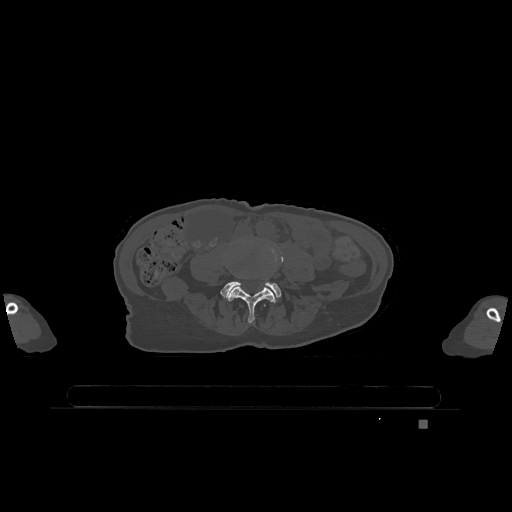
CT including the spine, one axial slice. Slice 276 of 1317 in the series (ordered by position). Bone window (W 1800 / L 400 HU). 0.5 mm slice thickness. 512 × 512 image matrix, field of view 500 × 500 mm. Patient: female, 74 years. Case-level facts recorded for this patient, not image findings: primary cancer: lung; vertebrae with lytic lesions (as recorded): T1, T4, T5, T6, L4, L5.
Structures marked on this image (semi-automatic segmentation, software-assisted and operator-edited):
- L4 vertebra: bounding box (x1, y1, x2, y2) in pixels: (228, 247, 283, 323)
- L5 vertebra: (221, 281, 281, 301)